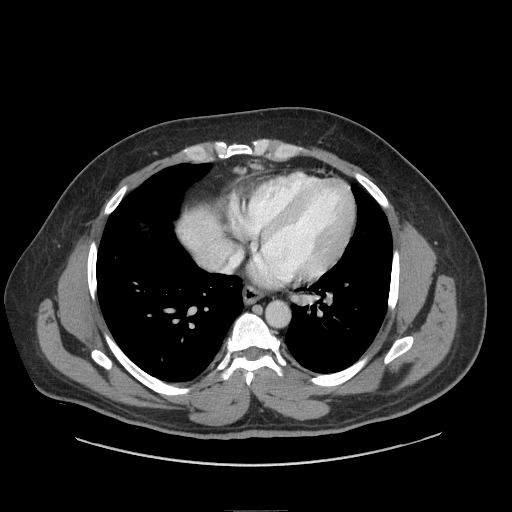
Contrast-enhanced abdominal CT (liver protocol), one axial slice; slice 79 of 87 in the series (ordered by position); reconstruction kernel STANDARD; soft-tissue window (W 400 / L 40 HU); 2.5 mm slice thickness; 512 × 512 image matrix. From the clinical record (not read from this slice): diagnosis: hepatocellular carcinoma (patient treated with transarterial chemoembolisation; whether this scan precedes or follows treatment is not stated here); TNM stage (as recorded): Stage-II; Child-Pugh class: A; tumour differentiation: moderately differentiated.
Outlined on this slice (semi-automatic segmentation, software-assisted and operator-edited):
- abdominal aorta: bounding box <266,301,290,327> (left, top, right, bottom; pixels)
- liver parenchyma outside the tumour (the mass and vessels are separate outlines, so this box may not span the whole liver): <178,210,222,254>